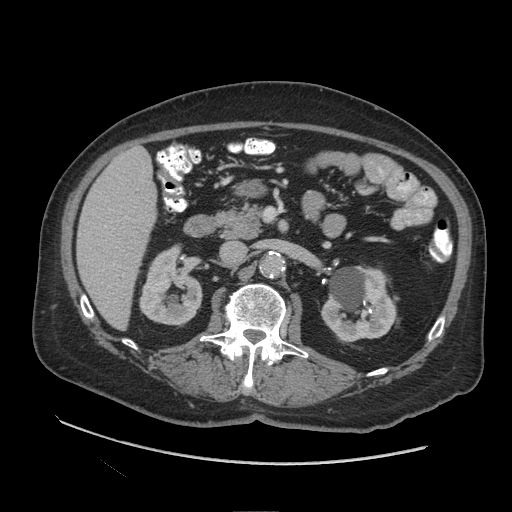
Contrast-enhanced abdominal CT (liver protocol), one axial slice. Slice 40 of 109 in the series (ordered by position). 140 kVp. Soft-tissue window (W 400 / L 40 HU). 2.5 mm slice thickness. 512 × 512 image matrix, field of view 420 × 420 mm. From the clinical record (not read from this slice): diagnosis: hepatocellular carcinoma (patient treated with transarterial chemoembolisation; whether this scan precedes or follows treatment is not stated here); TNM stage (as recorded): Stage-I.
Structures marked on this image (semi-automatic segmentation, software-assisted and operator-edited):
- liver parenchyma outside the tumour (the mass and vessels are separate outlines, so this box may not span the whole liver): bounding box <76,148,156,328> (left, top, right, bottom; pixels)
- liver vessels: <105,208,111,227>